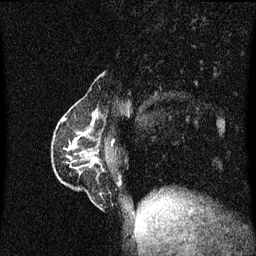
Breast MRI (dynamic contrast-enhanced), one sagittal slice; position 18 of 60 along the scan axis; dynamic contrast-enhanced series, image 2 of 3 at this slice position (ordered by acquisition); 1.5 T; TE 4.2 ms, TR 8.4 ms; 2 mm slice thickness; 256 × 256 image matrix. Female patient, age 40 years.
Annotated regions visible in this slice (semi-automatic segmentation, software-assisted and operator-edited):
- analysis volume of interest (the breast-tissue region the enhancement analysis was run in; not a lesion): bounding box <57,110,109,189> (left, top, right, bottom; pixels)
- tumour enhancement mask (voxels above the 70 % enhancement threshold inside the analysis volume of interest): <61,116,96,159>